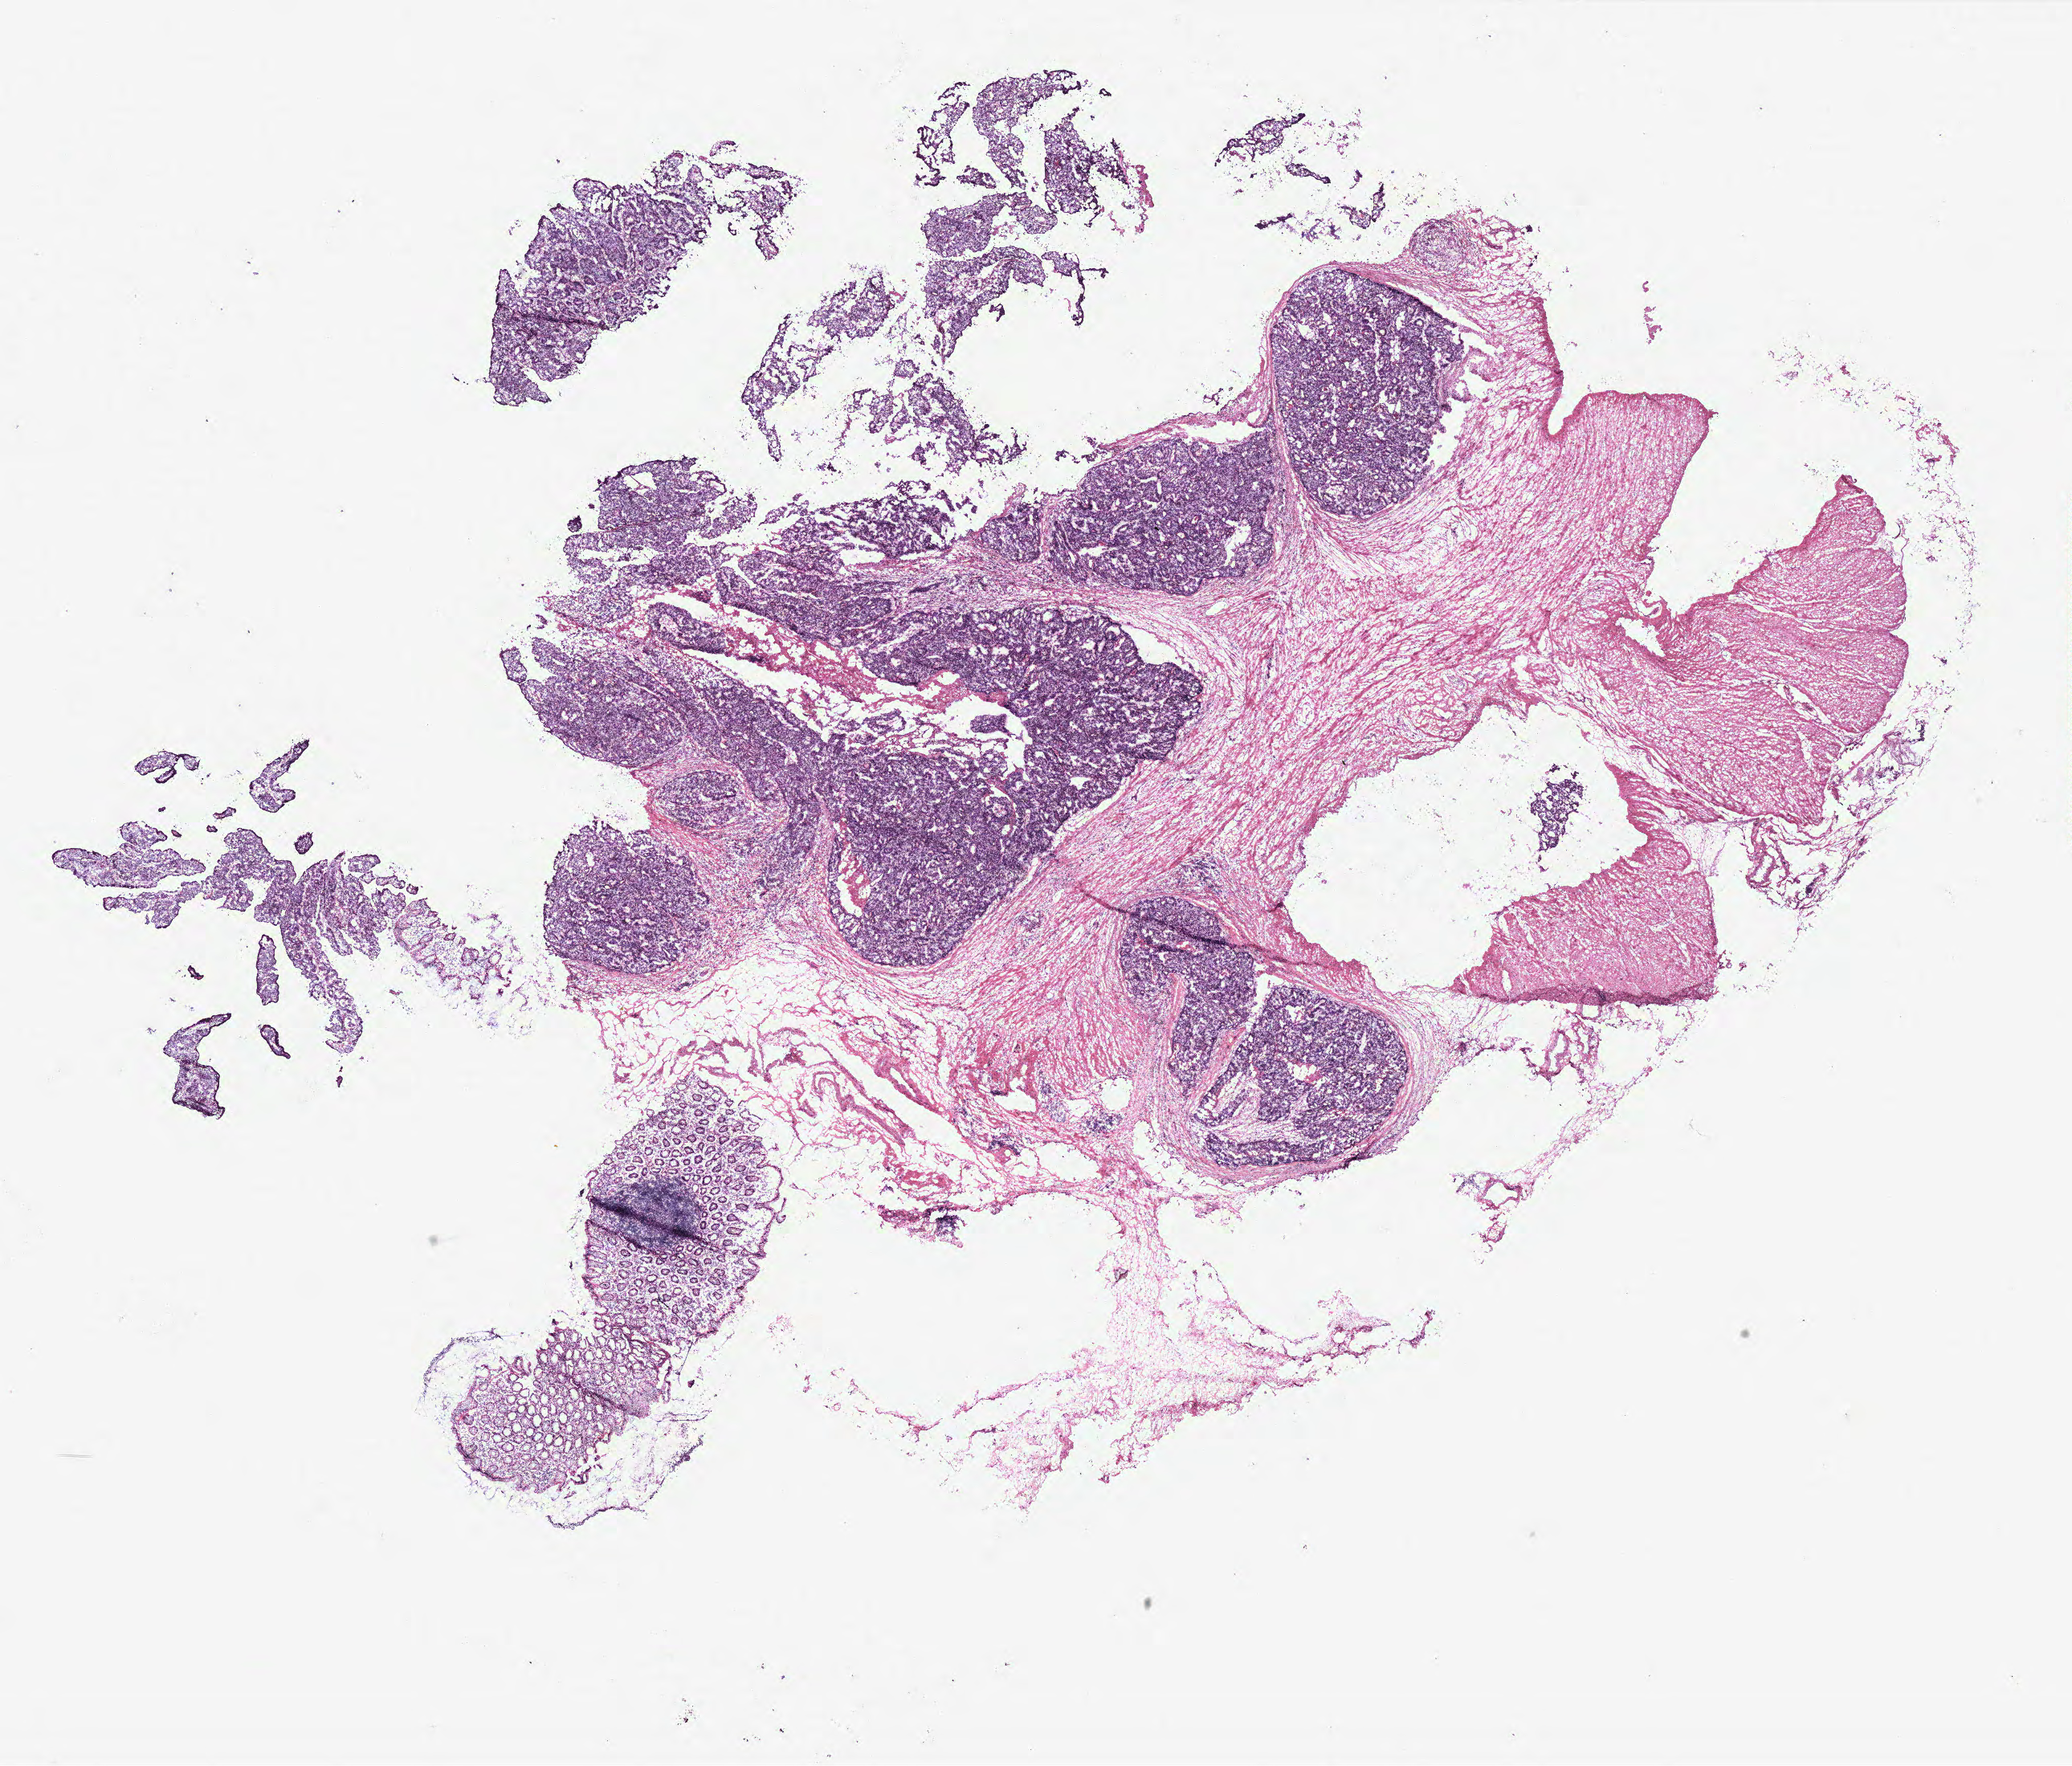
H&E-stained whole-slide image, a low-resolution overview of the entire scanned area, about 20.6 x 17.6 mm (slide scanned at 40x), colon, tumour tissue. Patient: female, age 67 years.
AJCC pathologic stage: IIA. Primary tumour site (as recorded): colon. Histologic diagnosis: Adenocarcinoma, NOS.